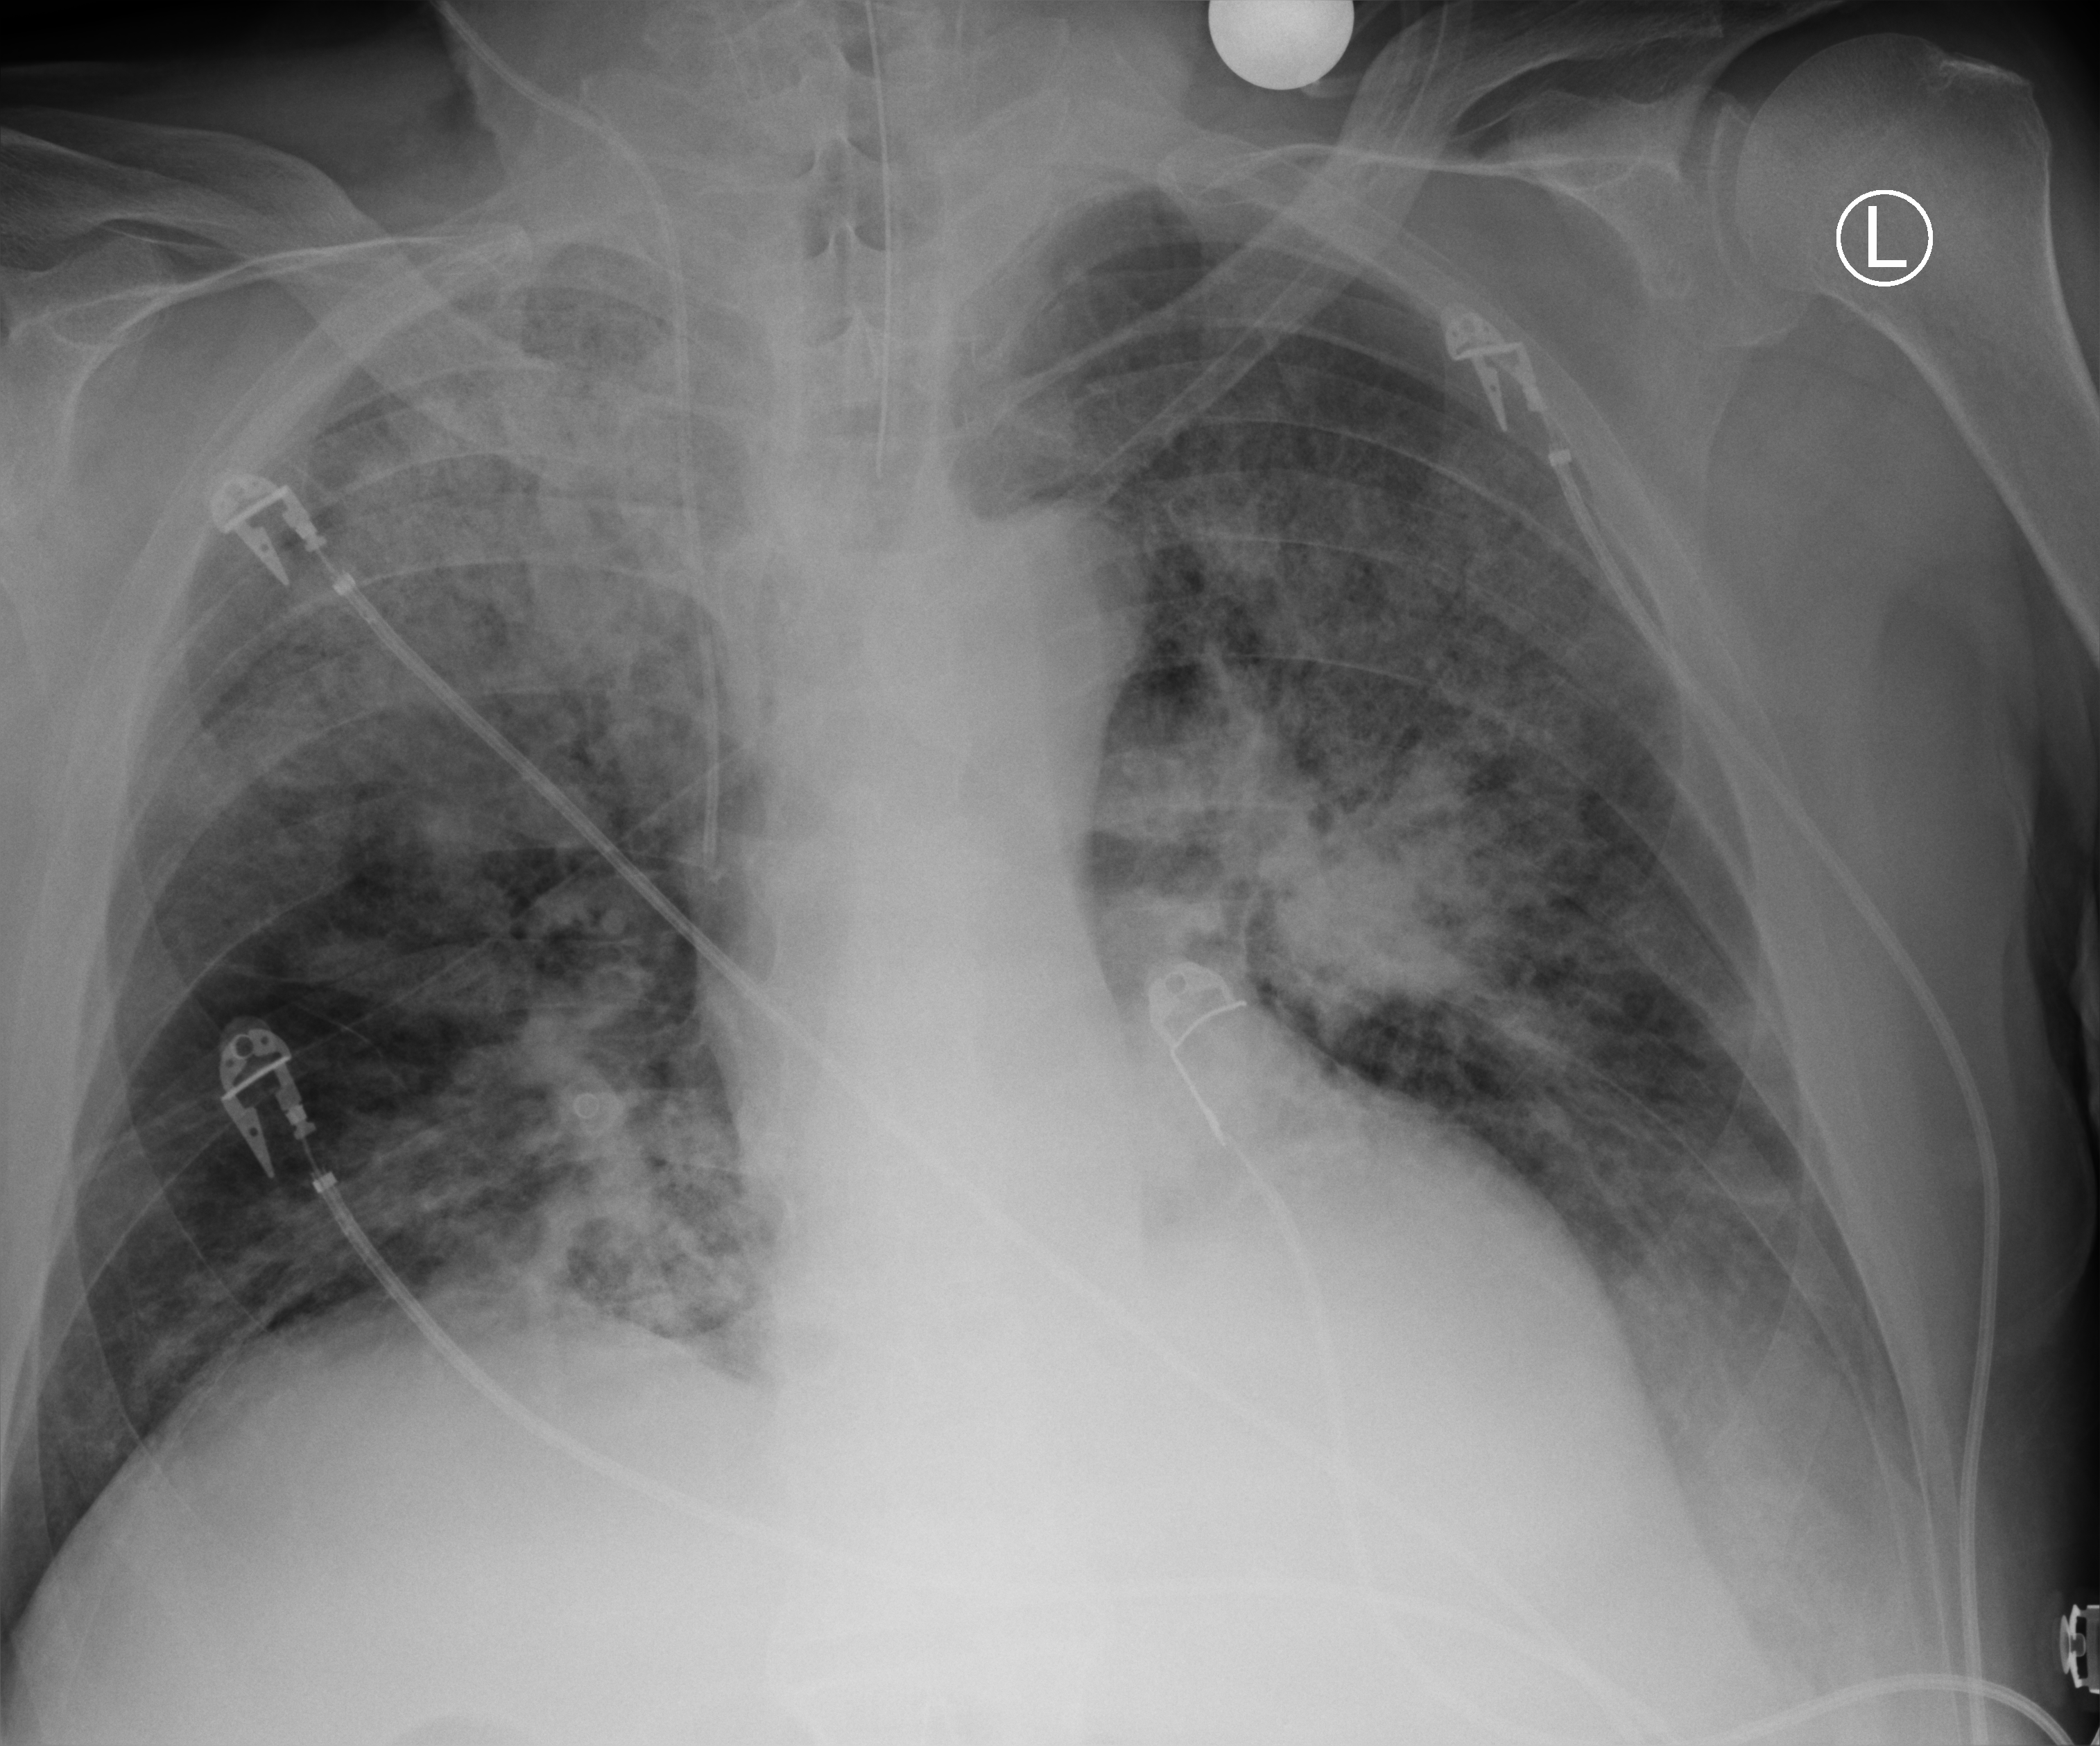
Portable chest radiograph, anteroposterior (AP) projection. Male patient hospitalised with COVID-19, age 75–90 years.
Hospital-stay facts (about this admission, not read from this image; timing relative to this image not recorded):
- length of hospital stay: 2 days